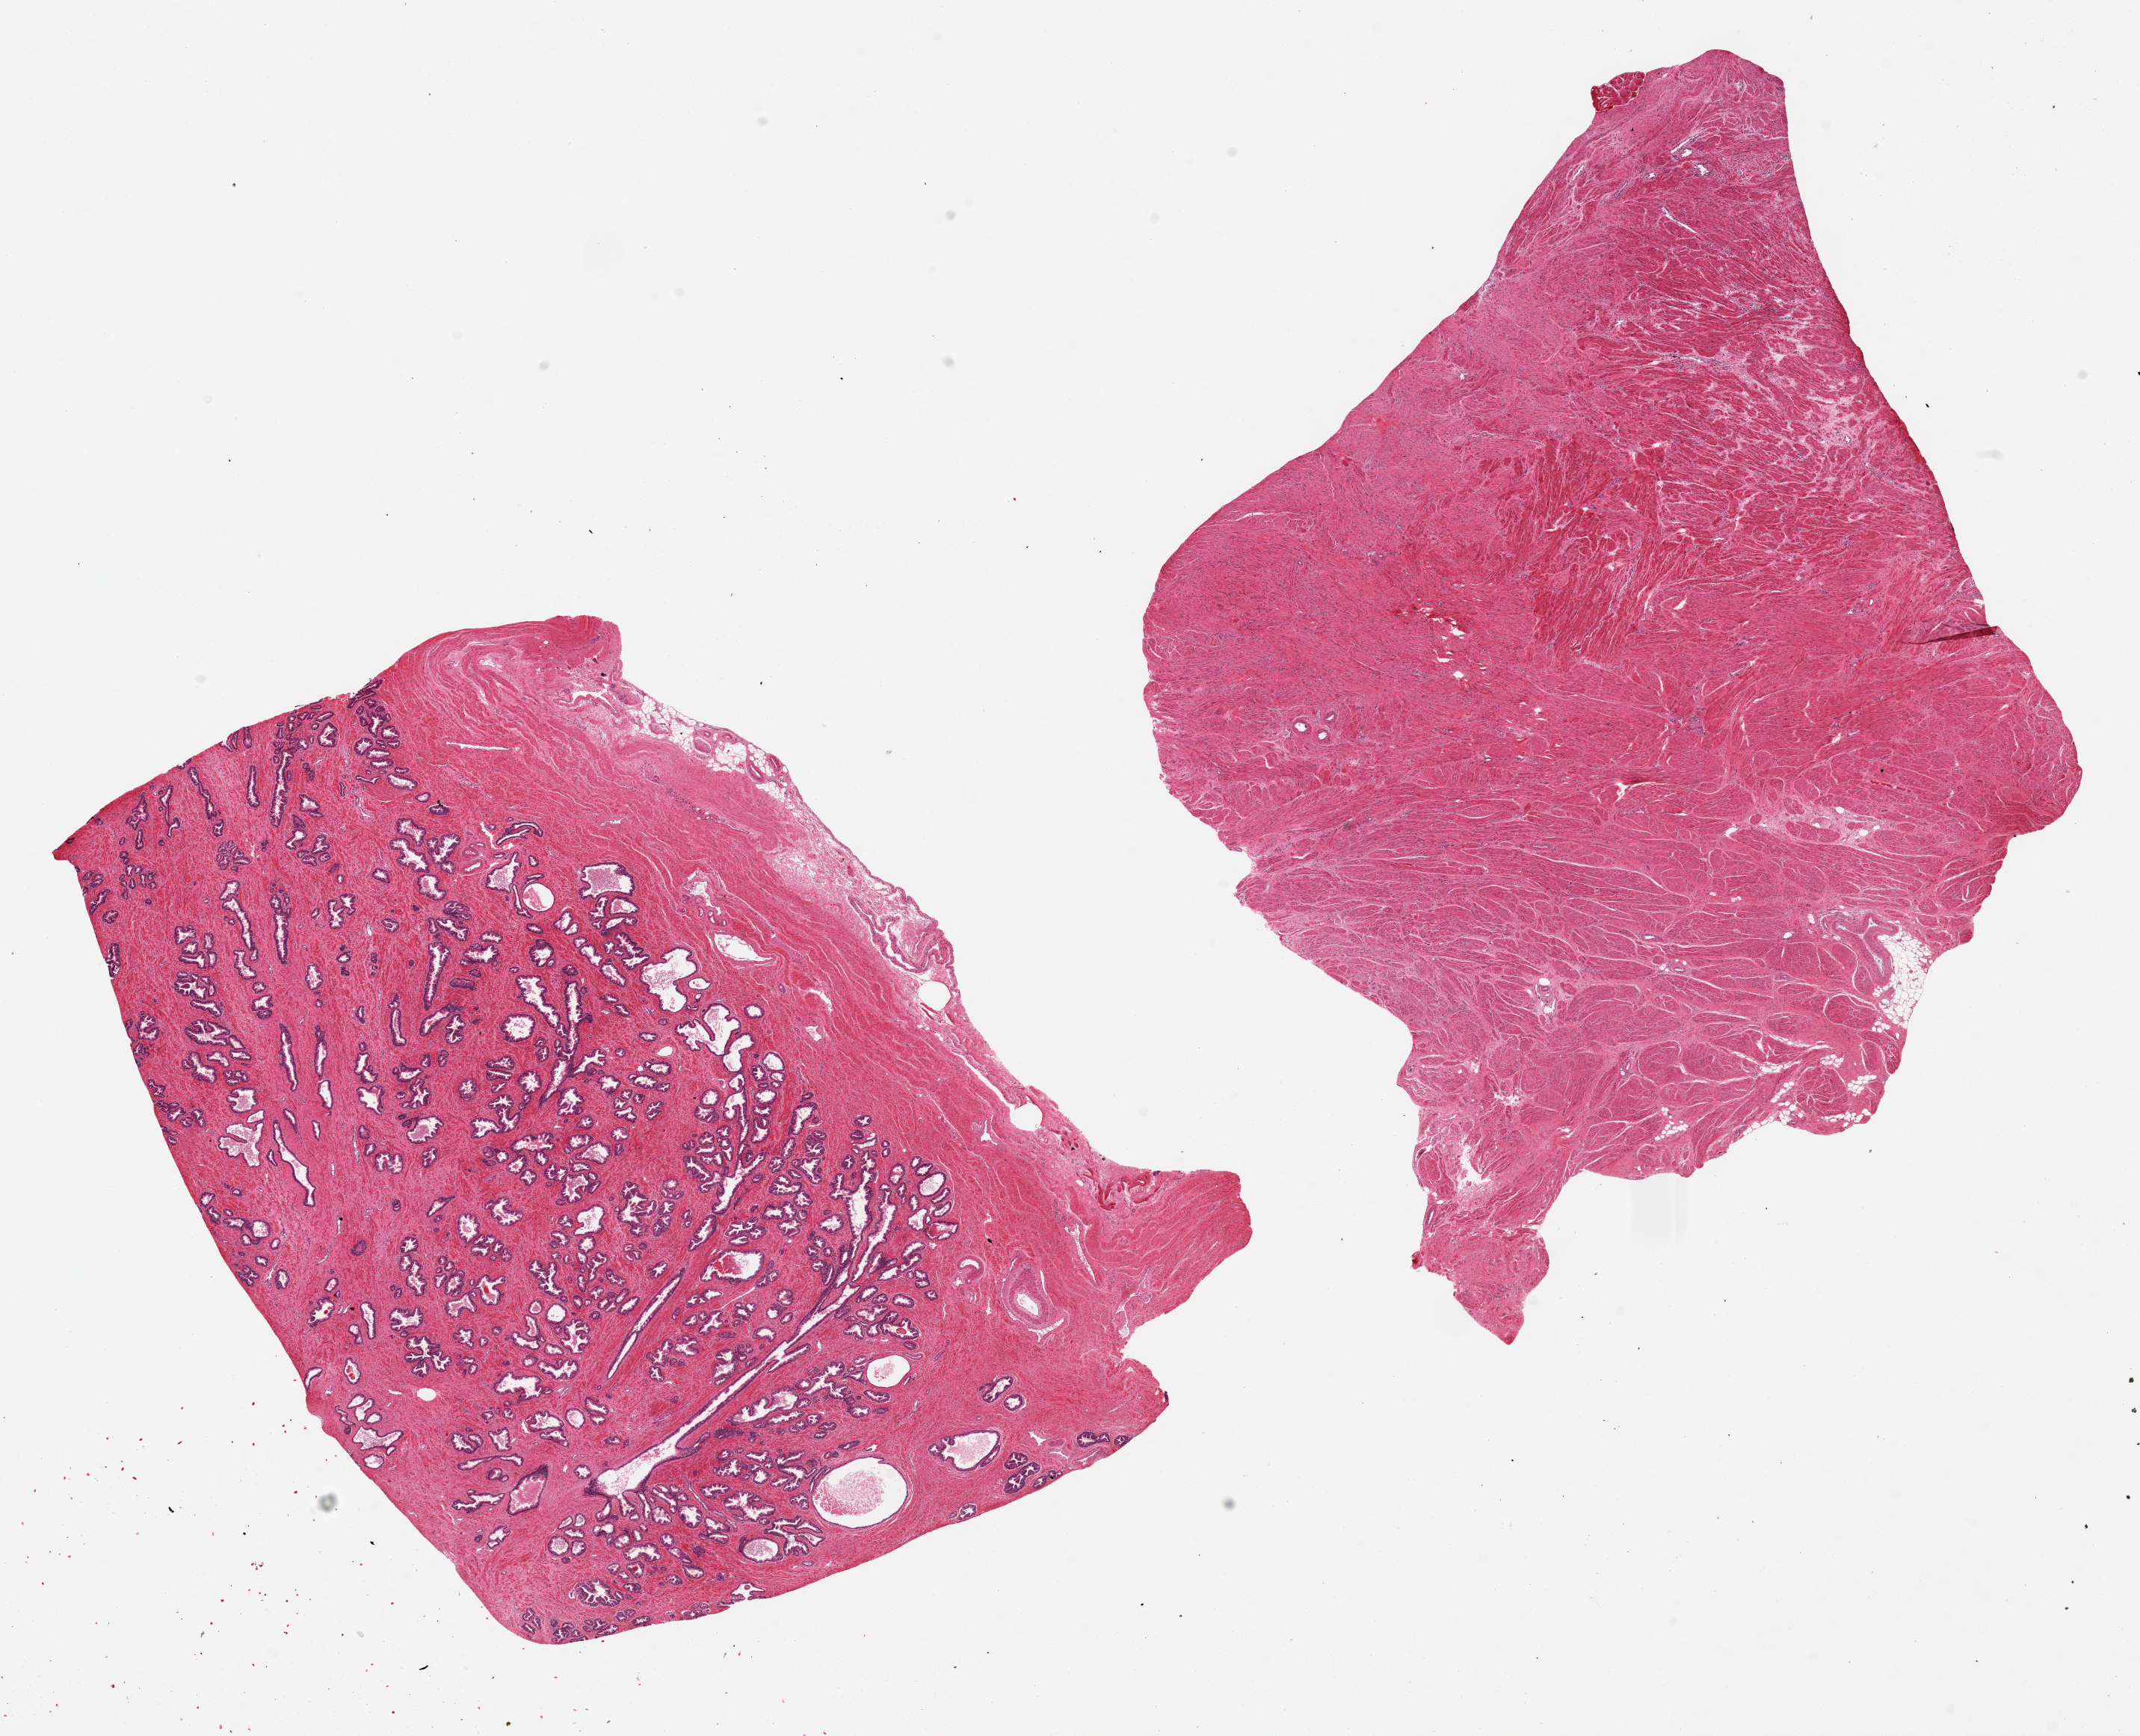
Digitized hematoxylin and eosin (H&E)-stained section — shown as a low-resolution overview of the whole scanned area (about 22.6 x 18.4 mm), PAXgene-fixed, paraffin-embedded tissue, section of prostate (target tissue), donor tissue sample. Male donor.
Pathologist's review note for this sample: 2 pieces, 10.7x8 & 9x8.6 mm; 1 has excellent glandular tissue, the other is all muscular stroma.